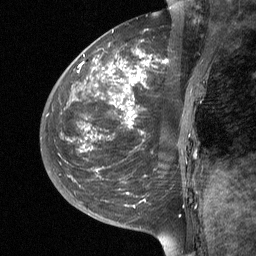
Breast MRI (dynamic contrast-enhanced), one sagittal slice; slice 16 of 64 in the series (ordered by position); dynamic contrast-enhanced study with each time point stored as its own series, time point 2 of 3 at this slice position (early post-contrast, ordered by acquisition time); 1.5 T; TE 4.8 ms, TR 27 ms; 2 mm slice thickness; 256 × 256 image matrix. Patient: female, 42 years. Case-level facts recorded for this patient, not image findings: setting: breast cancer imaged before/during neoadjuvant chemotherapy; receptor status: triple-negative.
Outlined on this slice (semi-automatically segmented with operator editing):
- analysis volume of interest (the breast-tissue region the enhancement analysis was run in; not a lesion): box from (x=43, y=29) to (x=203, y=190) px
- tumour enhancement mask (voxels above the 90 % enhancement threshold inside the analysis volume of interest): (x=79, y=49)–(x=150, y=149)